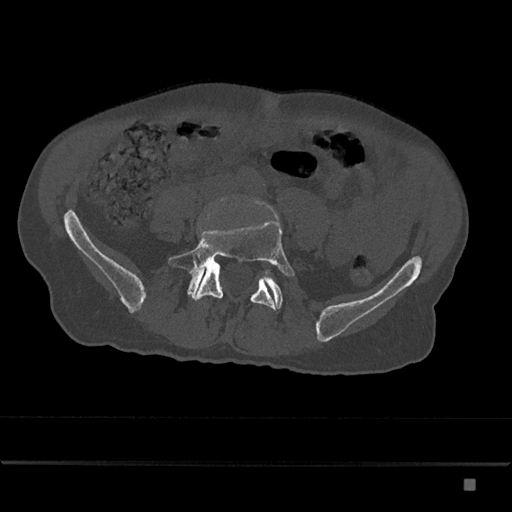
CT including the spine, one axial slice; position 278 of 797 along the scan axis; reconstruction kernel Br40s/3; 120 kVp; bone window (W 1800 / L 400 HU); 0.5 mm slice thickness; 512 × 512 image matrix. Male patient, age 72 years. Case-level facts recorded for this patient, not image findings: primary cancer: prostate.
Structures marked on this image (semi-automatic segmentation, software-assisted and operator-edited):
- L5 vertebra: bounding box <168,203,295,310> (left, top, right, bottom; pixels)